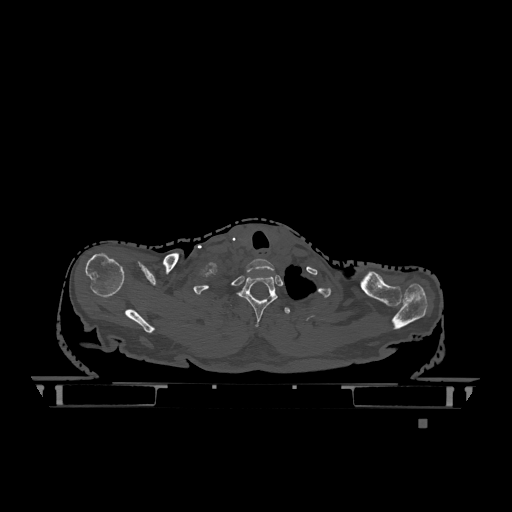
CT including the spine, one axial slice. Position 996 of 1317 along the scan axis. Bone window (W 1800 / L 400 HU). 0.5 mm slice thickness. 512 × 512 image matrix, field of view 500 × 500 mm. Female patient, age 74 years. Case-level facts recorded for this patient, not image findings: primary cancer: lung; vertebrae with lytic lesions (as recorded): T1, T4, T5, T6, L4, L5.
Annotated regions visible in this slice (semi-automatically segmented with operator editing):
- T1 vertebra: bounding box [x1, y1, x2, y2] px = [238, 275, 278, 327]
- T2 vertebra: [285, 307, 290, 314]